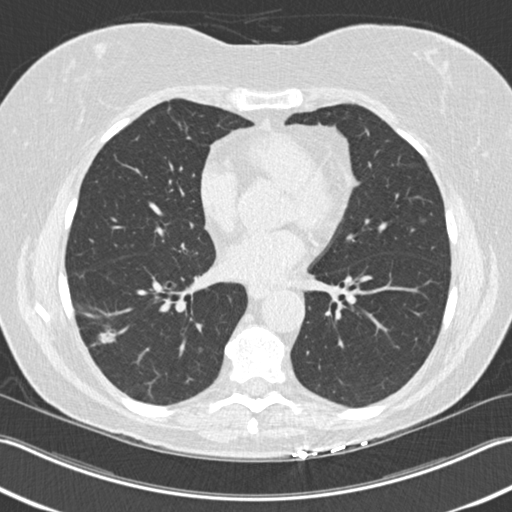
Axial slice from a low-dose chest CT screening exam. Baseline annual screen. Lung window (W 1500 / L -600 HU). 2 mm slice thickness. Slice 106 of 211 in the series. 512 × 512 image matrix, field of view 348 × 348 mm. Female participant, aged 63 years at enrolment. Current smoker at enrolment.
Expert-annotated lung lesion, bounding box [x1, y1, x2, y2] px = [65, 306, 131, 369]. The screening reader recorded 3 non-calcified nodules or masses ≥4 mm on this exam; which of them this box marks is not recorded. Later outcome: lung cancer diagnosed 57 days after this screen — bronchiolo-alveolar adenocarcinoma, NOS, right lower lobe, well differentiated (G1), stage IA (AJCC 6th edition), 25 mm at pathology.